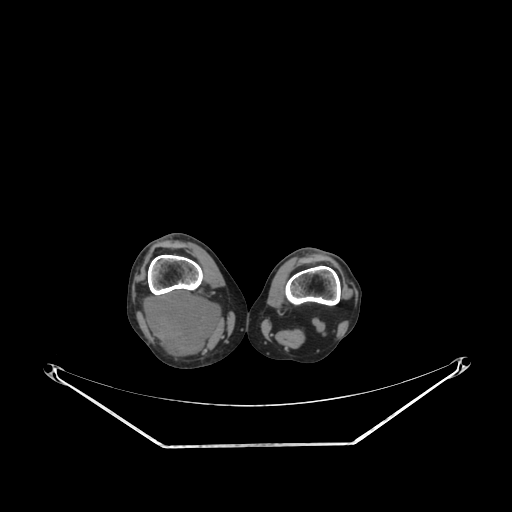
CT of an extremity soft-tissue mass (from a PET/CT study), one axial slice. Slice 177 of 267 in the series (ordered by position). Reconstruction kernel SOFT. Soft-tissue window (W 400 / L 40 HU). 512 × 512 image matrix. Female patient. From the clinical record (not read from this slice): histological type: liposarcoma; site of the primary tumour: right thigh.
Annotated regions visible in this slice (expert contour drawn on MRI and transferred to this co-registered scan by the dataset authors):
- gross tumour volume (mass): bounding box [x1, y1, x2, y2] px = [144, 290, 222, 357]